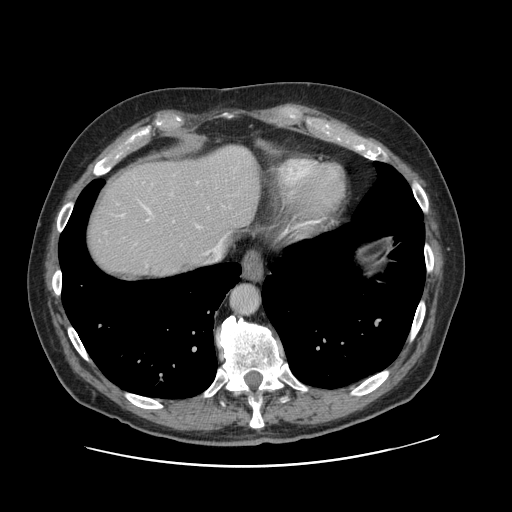
Contrast-enhanced abdominal CT, one axial slice; slice 103 of 138 in the series (ordered by position); 120 kVp; intravenous contrast given; soft-tissue window (W 400 / L 40 HU); 512 × 512 image matrix, field of view 402 × 402 mm. Male patient, age 71 years. Case-level facts recorded for this patient, not image findings: diagnosis: colorectal cancer liver metastases, imaged before liver resection; multiple liver metastases: no; largest metastasis: 3.3 cm; disease in both lobes: no.
Annotated regions visible in this slice (expert manual segmentation):
- hepatic veins: bounding box <145,207,226,264> (left, top, right, bottom; pixels)
- liver: <86,145,260,282>
- planned liver remnant (the part of the liver to remain after resection): <86,164,228,281>